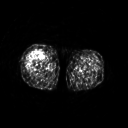
FDG PET of an extremity soft-tissue mass (from a PET/CT study), one axial slice; 3.27 mm slice thickness; 128 × 128 image matrix, field of view 500 × 500 mm. Patient: female, 57 years. From the clinical record (not read from this slice): histological type: pleiomorphic undifferentiated sarcoma; grade: high; site of the primary tumour: right quadricep.
Annotated regions visible in this slice (expert contour drawn on MRI and transferred to this co-registered scan by the dataset authors):
- tumour plus oedema (research contour): box from (x=26, y=51) to (x=42, y=69) px